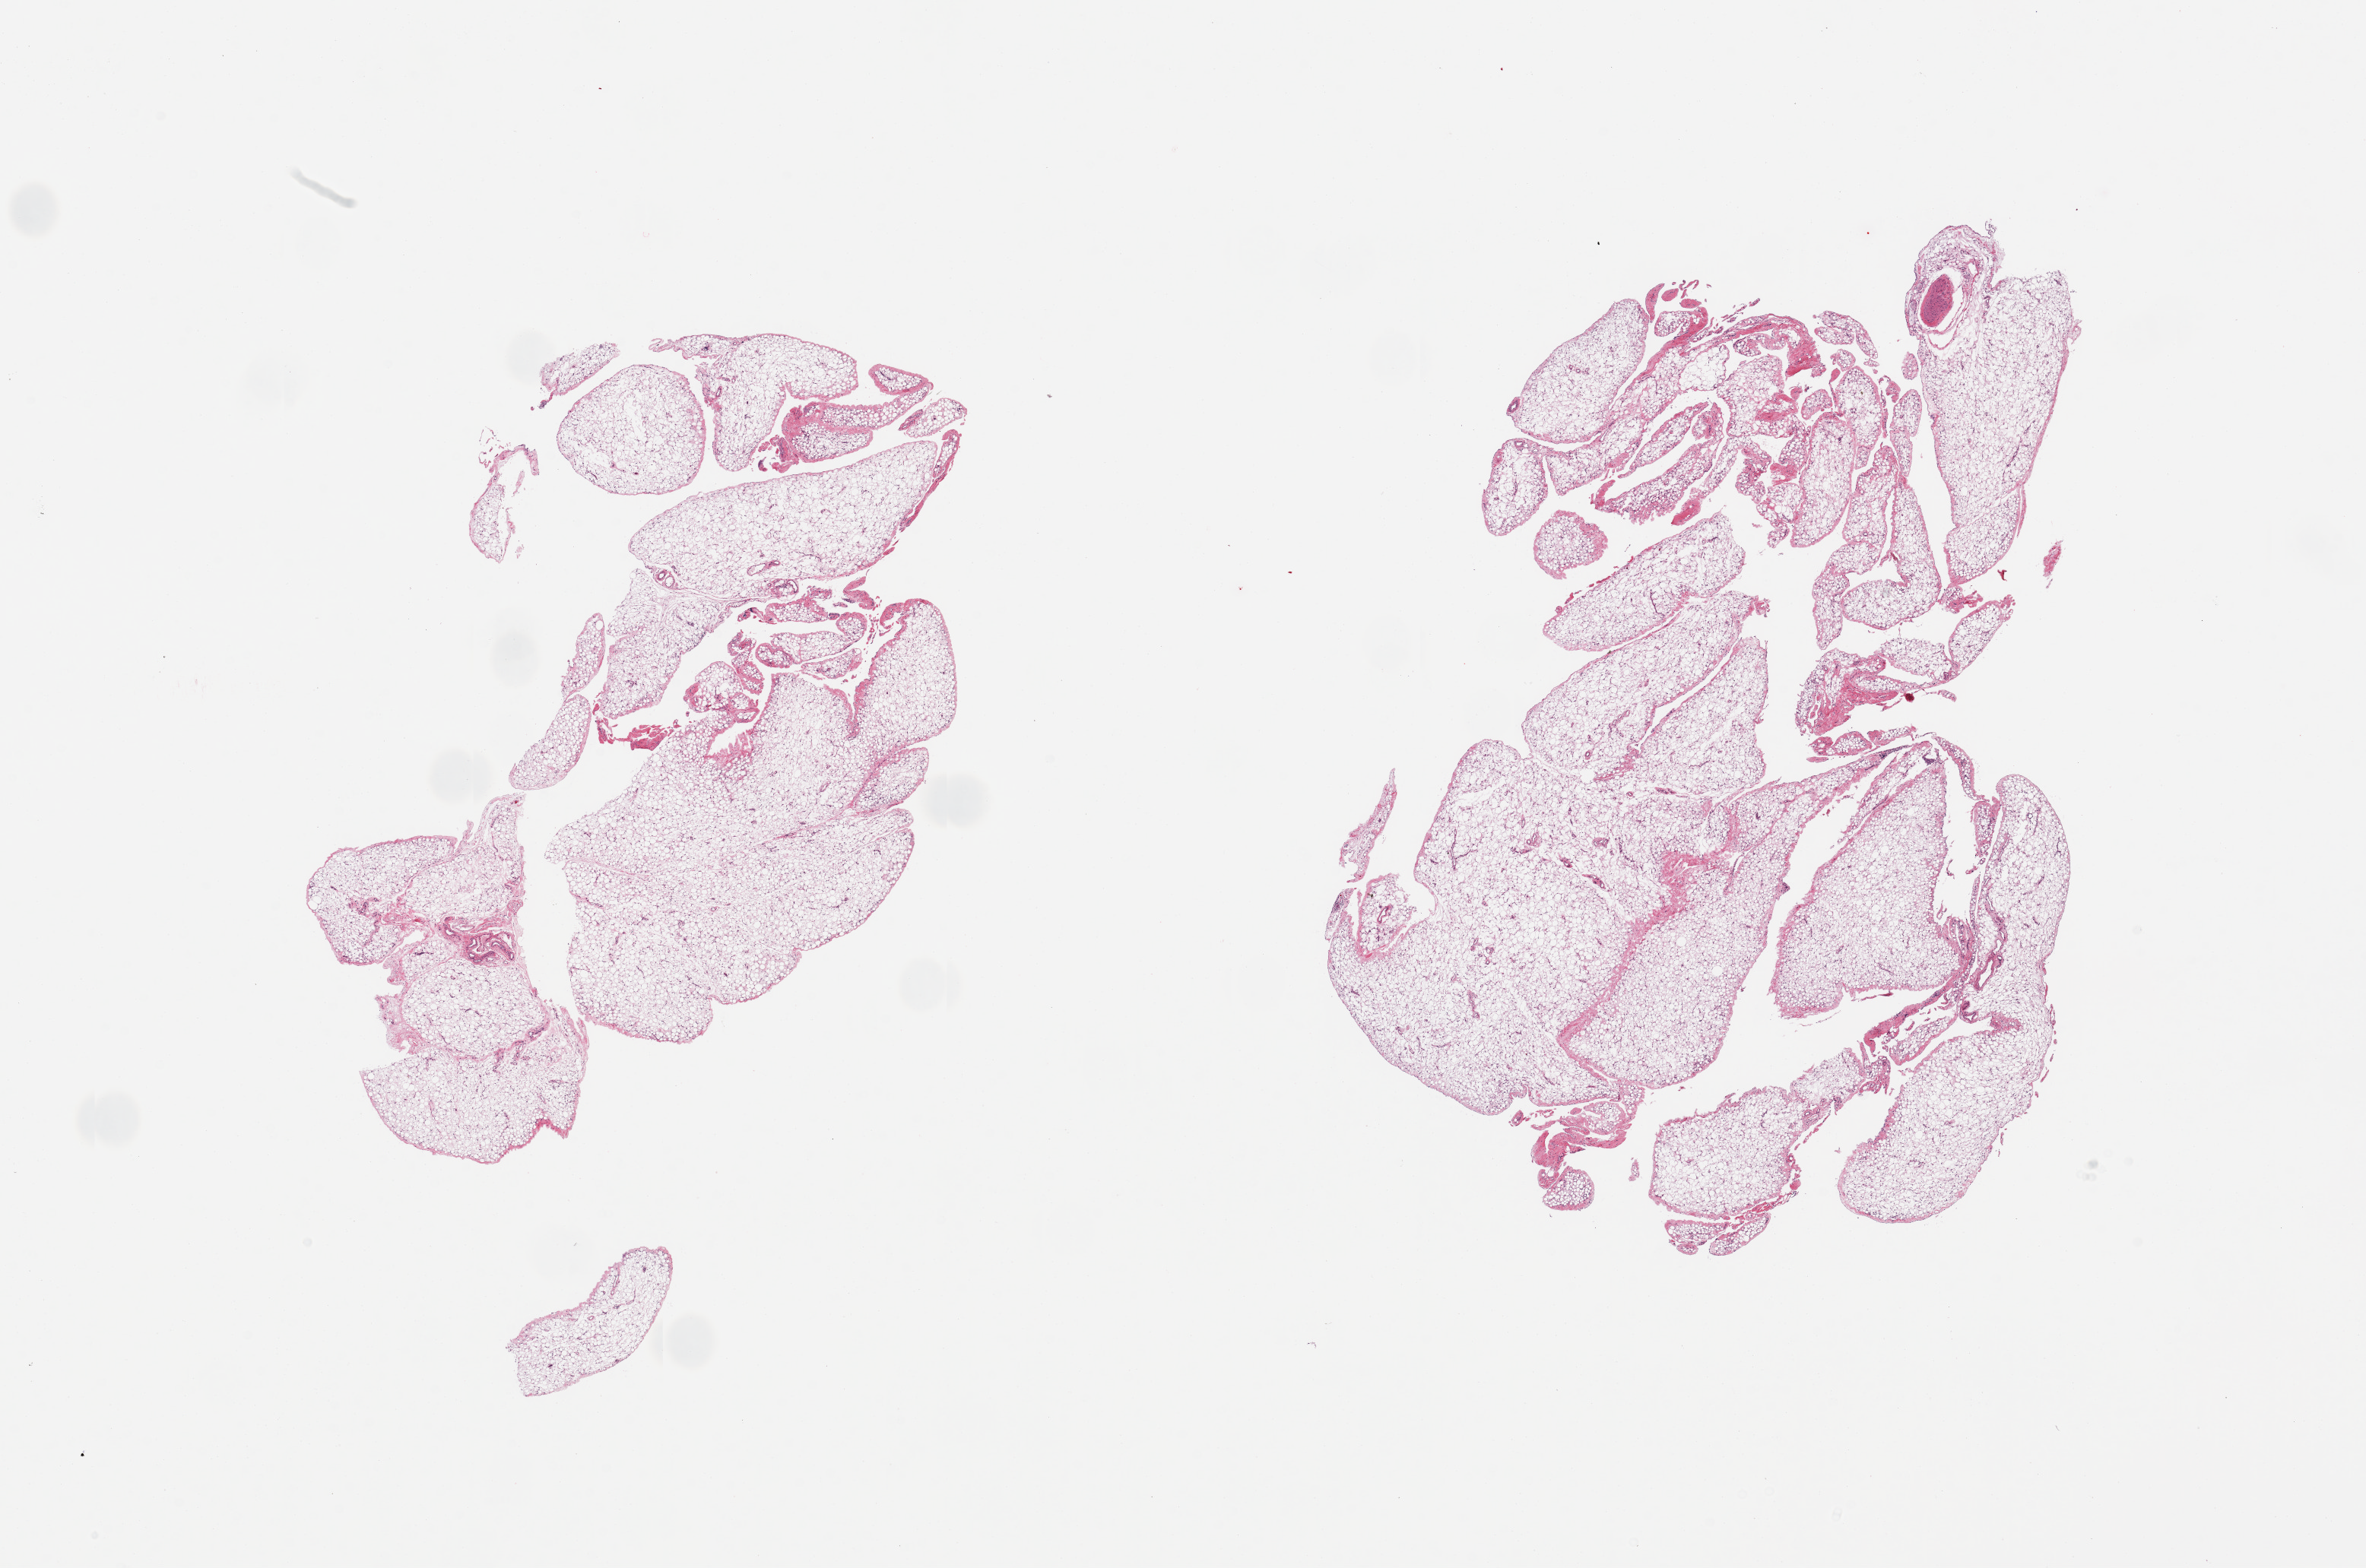
Whole-slide image, H&E stain, brightfield — shown as a low-resolution overview of the whole scanned area (about 24.6 x 16.3 mm), PAXgene-fixed, paraffin-embedded tissue, section of omentum (target tissue), donor tissue sample. Donor sex: male.
Reviewer comment on this tissue sample: 2 pieces; lobulated fat with minimal fibrous content.